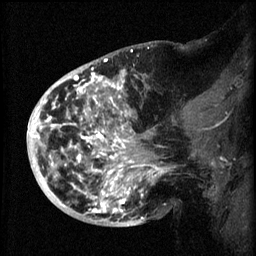
Breast MRI (dynamic contrast-enhanced), one sagittal slice; position 24 of 60 along the scan axis; 3 images stored at this slice position (order not interpretable as contrast timing); 1.5 T; TE 4.2 ms, TR 8.2 ms; 2 mm slice thickness; 256 × 256 image matrix, field of view 200 × 200 mm. Female patient, age 50 years.
Structures marked on this image (semi-automatic segmentation, software-assisted and operator-edited):
- analysis volume of interest (the breast-tissue region the enhancement analysis was run in; not a lesion): bounding box [x1, y1, x2, y2] px = [44, 72, 165, 219]
- tumour enhancement mask (voxels above the 70 % enhancement threshold inside the analysis volume of interest): [45, 72, 162, 219]